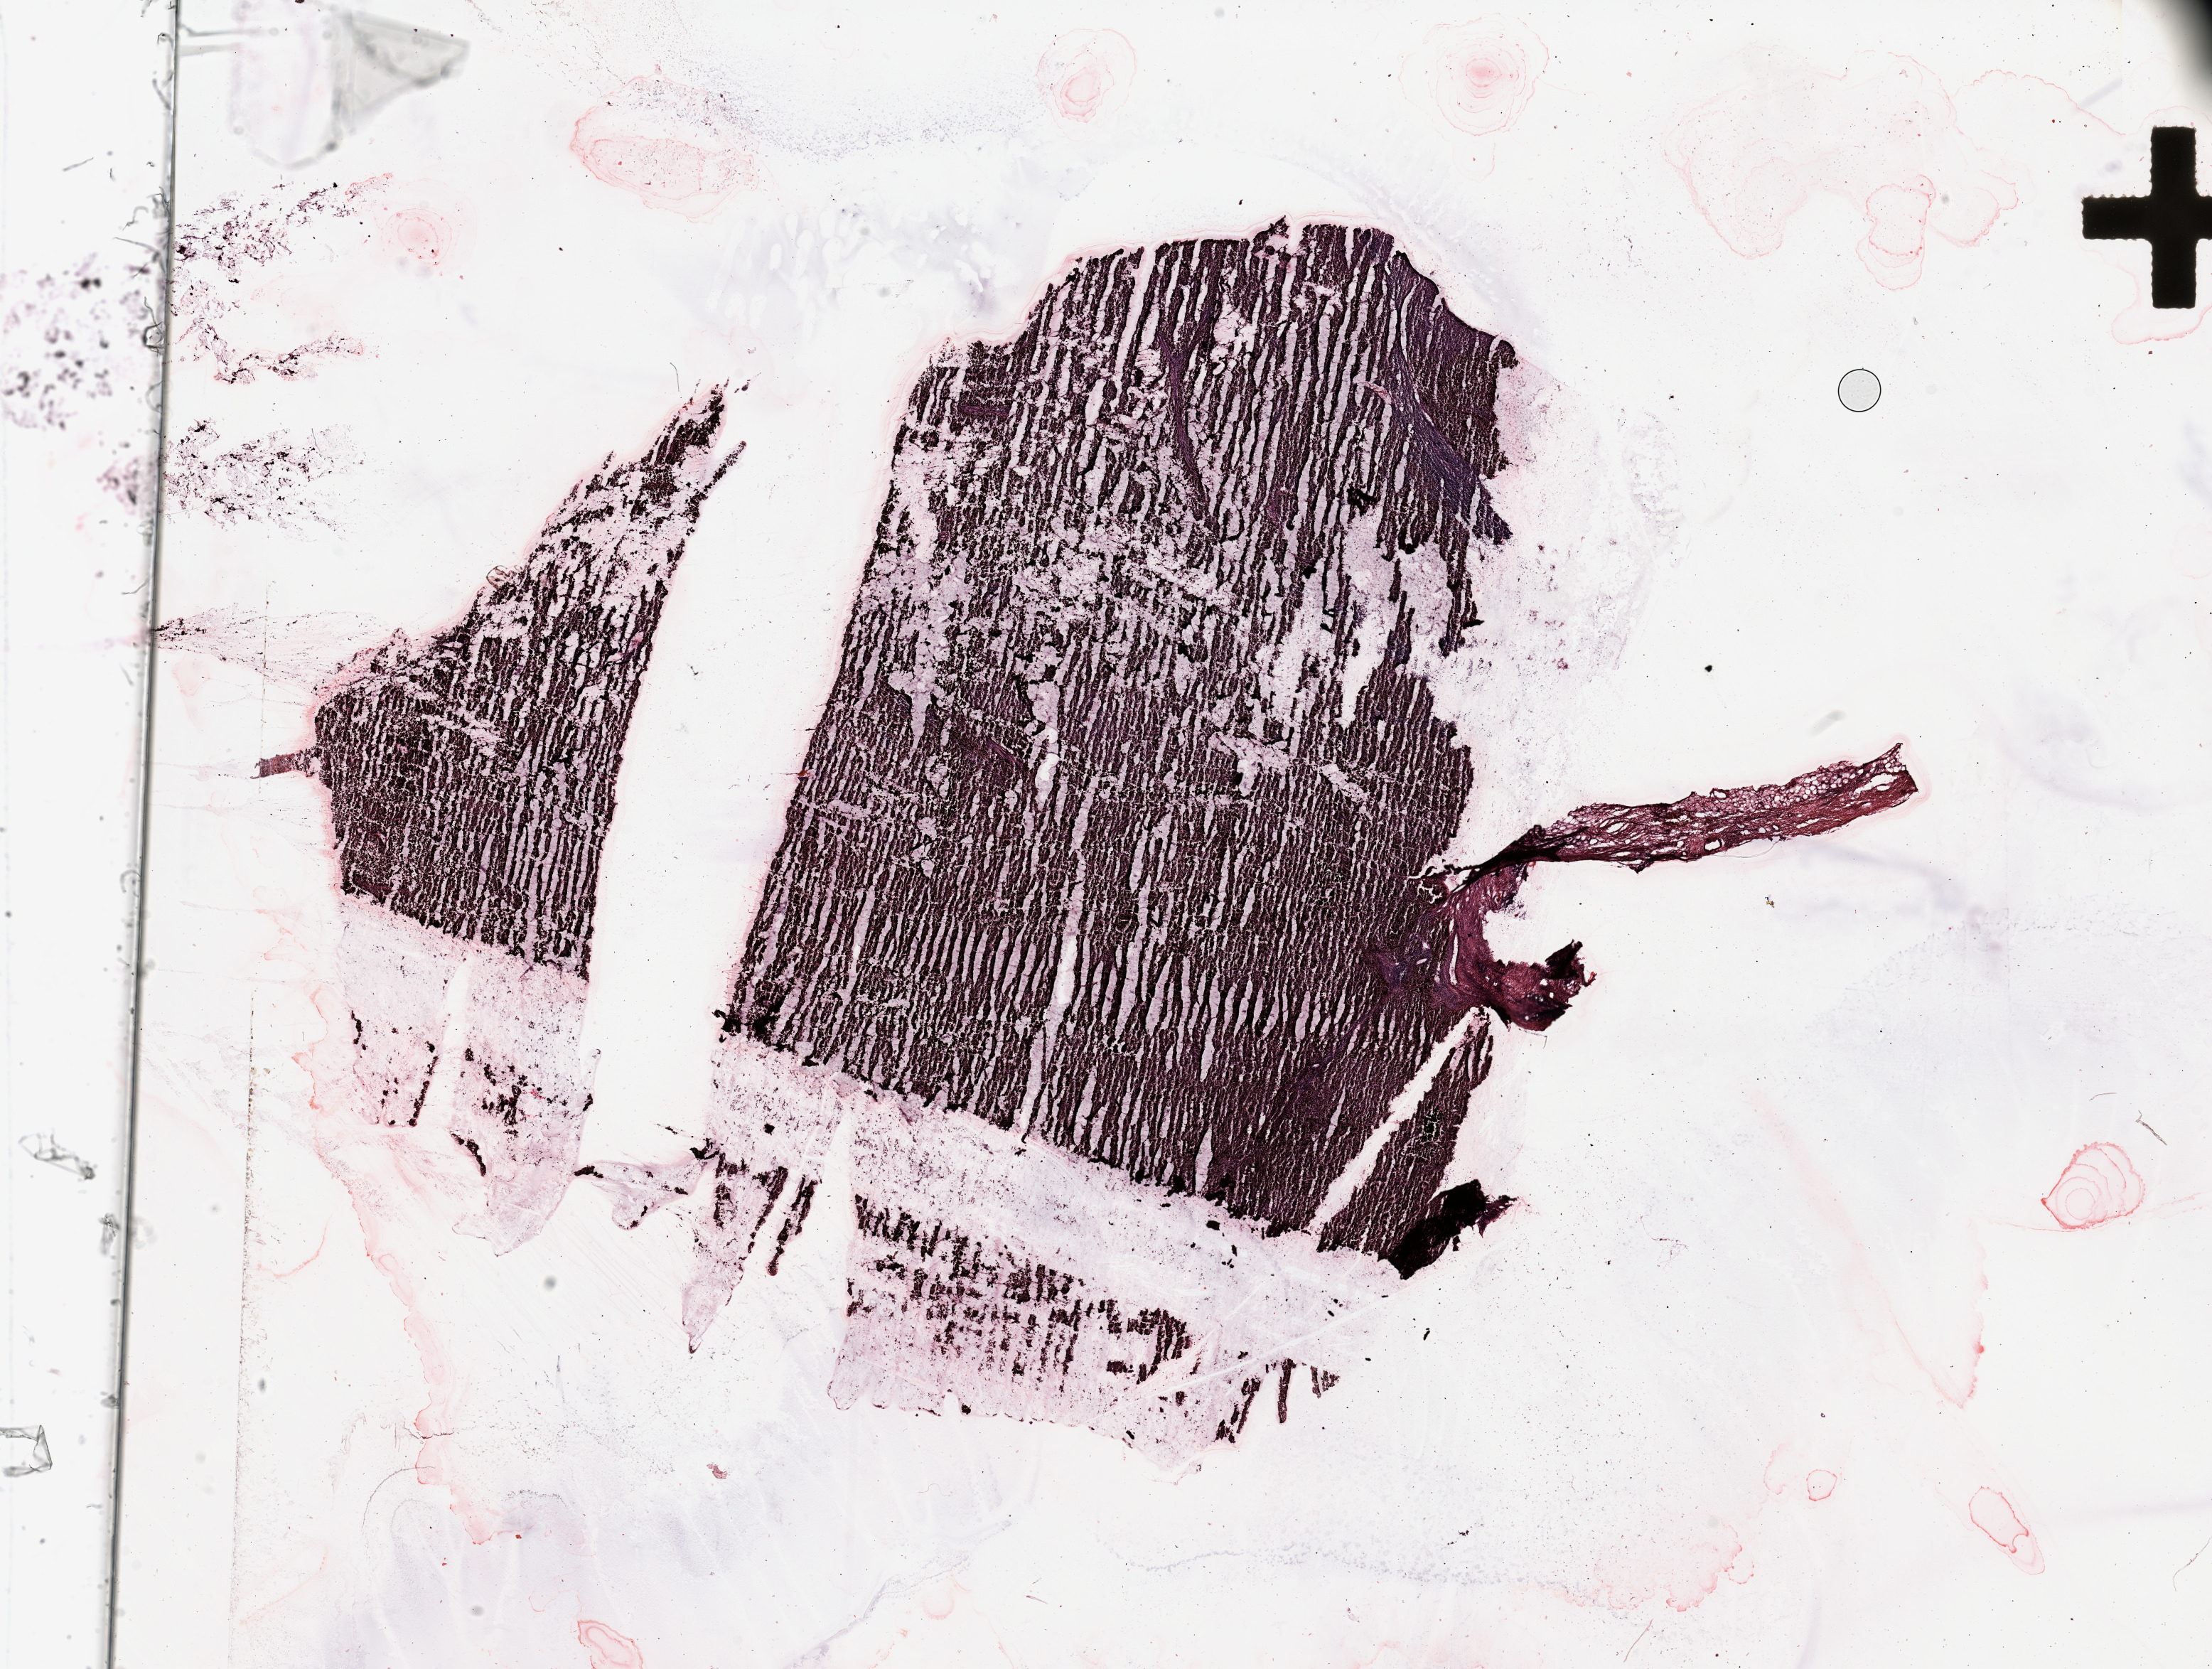
H&E whole-slide image — whole scanned area (about 24.6 x 18.6 mm, slide scanned at 20x) shown as a low-resolution overview. Melanoma tumour tissue; sampled site not recorded. Patient: female, age 74 years.
Primary tumour site (as recorded): trunk. Patient diagnosis (cohort enrolment): cutaneous melanoma (skin).